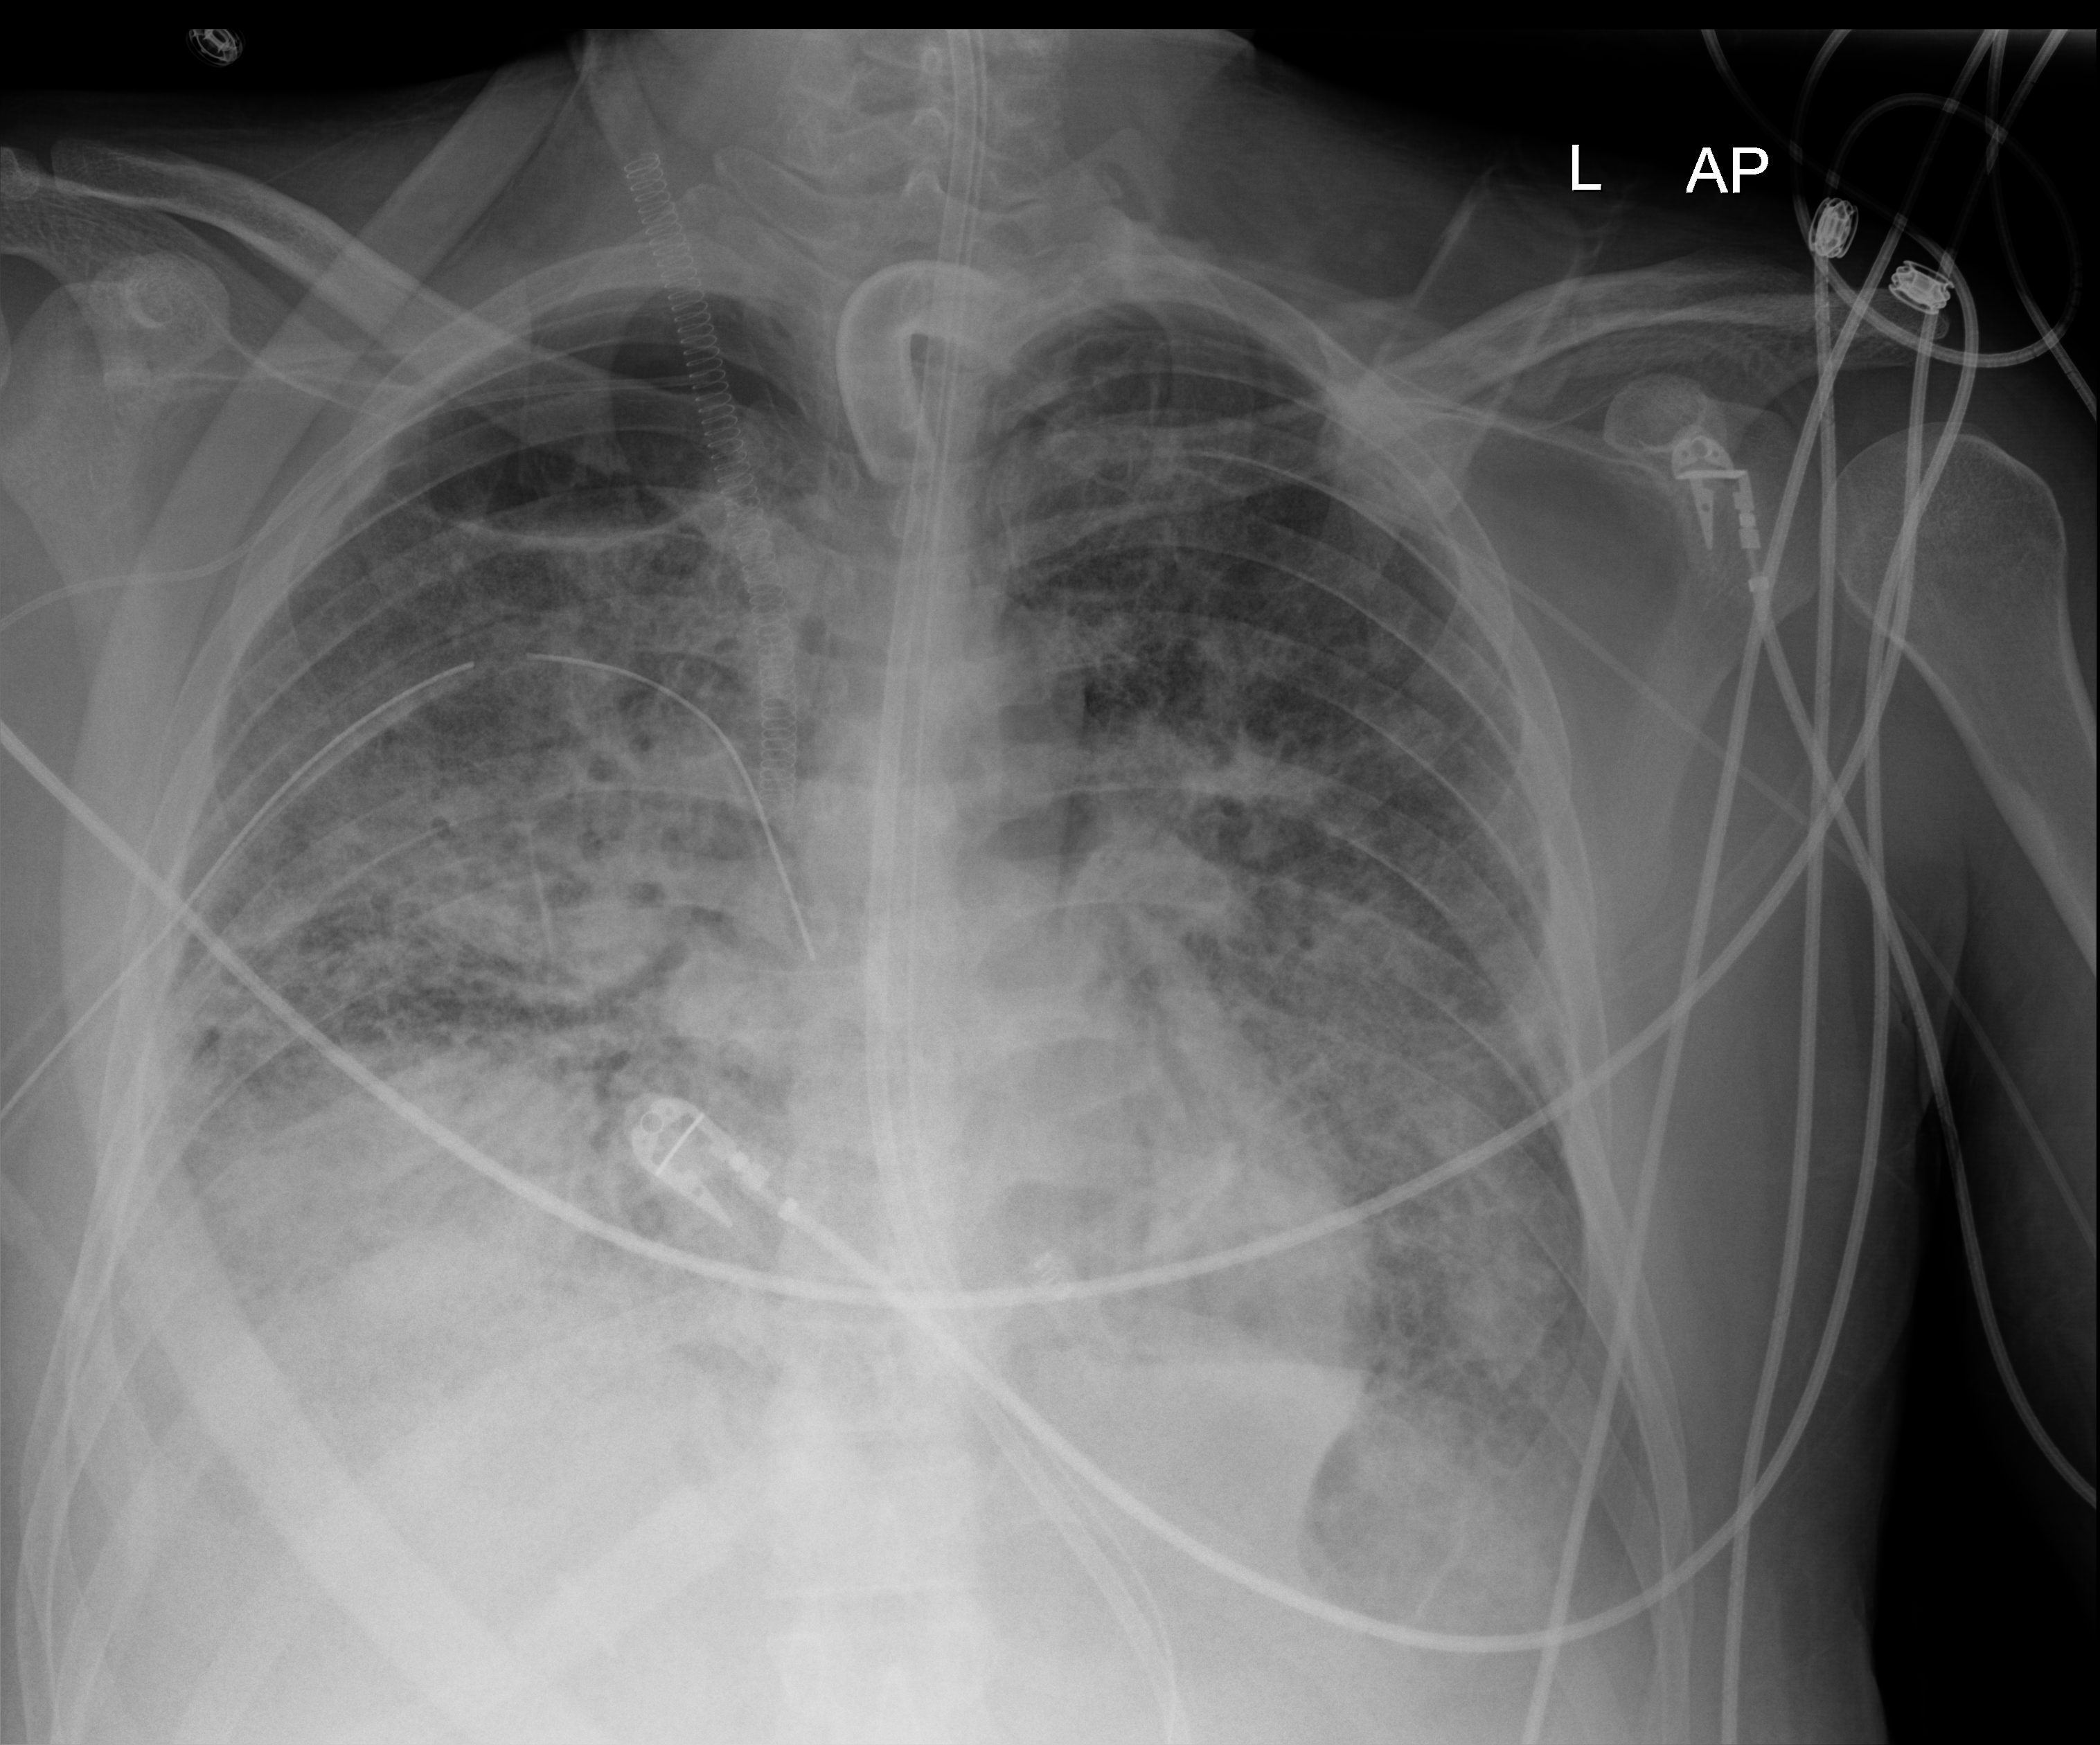
Chest radiograph; anteroposterior (AP) projection. Patient hospitalised with COVID-19, aged 18–59 years.
From the hospital-stay record, not from the radiograph (when in the stay this image was taken is not recorded): other chronic lung disease (admission record): no; admitted to intensive care during this hospital stay: yes; mechanically ventilated during this hospital stay: yes.